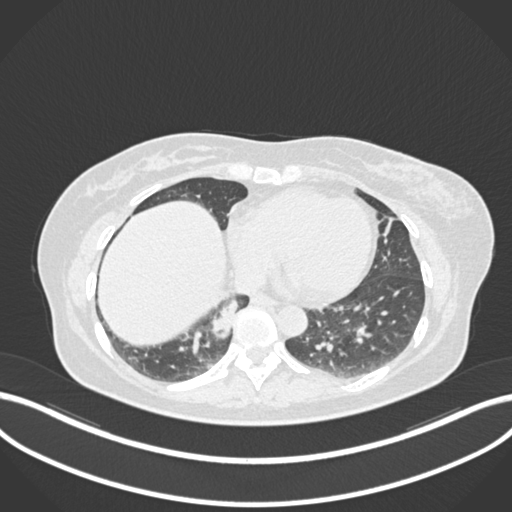
Chest CT, one axial slice. Position 545 of 677 along the scan axis. 120 kVp. Lung window (W 1500 / L -600 HU). 512 × 512 image matrix. Female patient, age 54 years. From the clinical record (not read from this slice): clinical TNM (as recorded): T4 N0 M0.
Structures marked on this image (rectangle marked by the reading radiologist):
- lung tumour (recorded histology: adenocarcinoma): bounding box (x1, y1, x2, y2) in pixels: (206, 295, 245, 341)